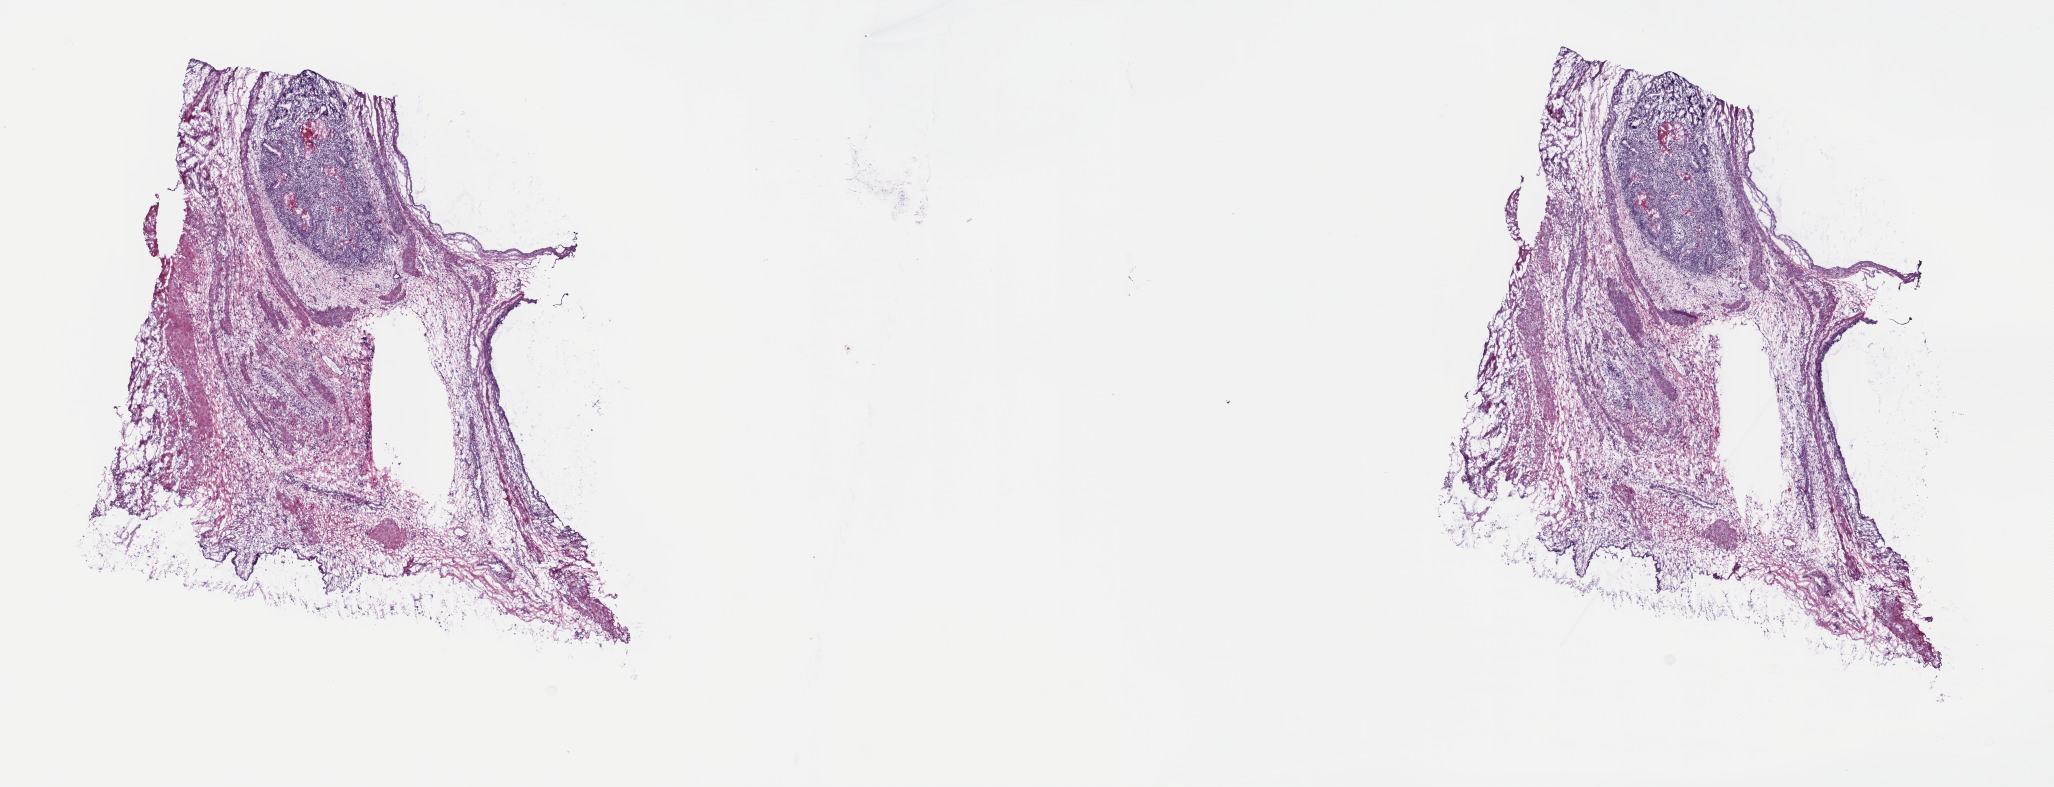
Hematoxylin and eosin (H&E) stained whole-slide image, a low-resolution overview of the entire scanned area, about 16.6 x 6.4 mm (acquisition: 40x scan), frozen section, testis, primary tumour sample. Male patient; age at initial diagnosis 36 years. Pathologist review of this section (percent, as recorded): tumour cells 70%, tumour nuclei 70%.
Pathologic diagnosis: Teratoma, benign.